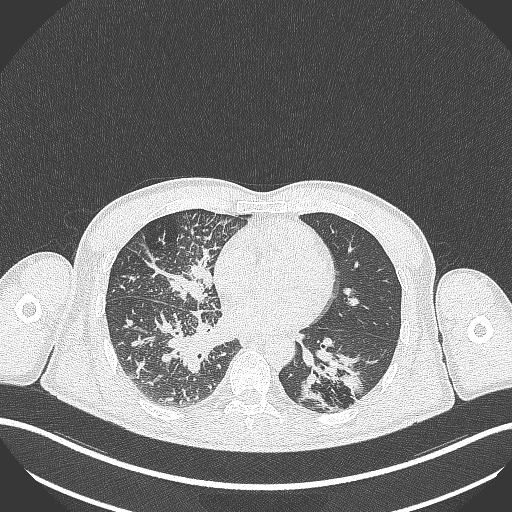
Chest CT, one axial slice. Position 135 of 348 along the scan axis. 120 kVp. Lung window (W 1500 / L -600 HU). 1 mm slice thickness. 512 × 512 image matrix, field of view 400 × 400 mm. Patient: male, 49 years. From the clinical record (not read from this slice): clinical TNM (as recorded): T2b N1 M0.
Outlined on this slice (bounding box drawn by a radiologist):
- lung tumour (recorded histology: adenocarcinoma): bounding box <297,341,368,412> (left, top, right, bottom; pixels)